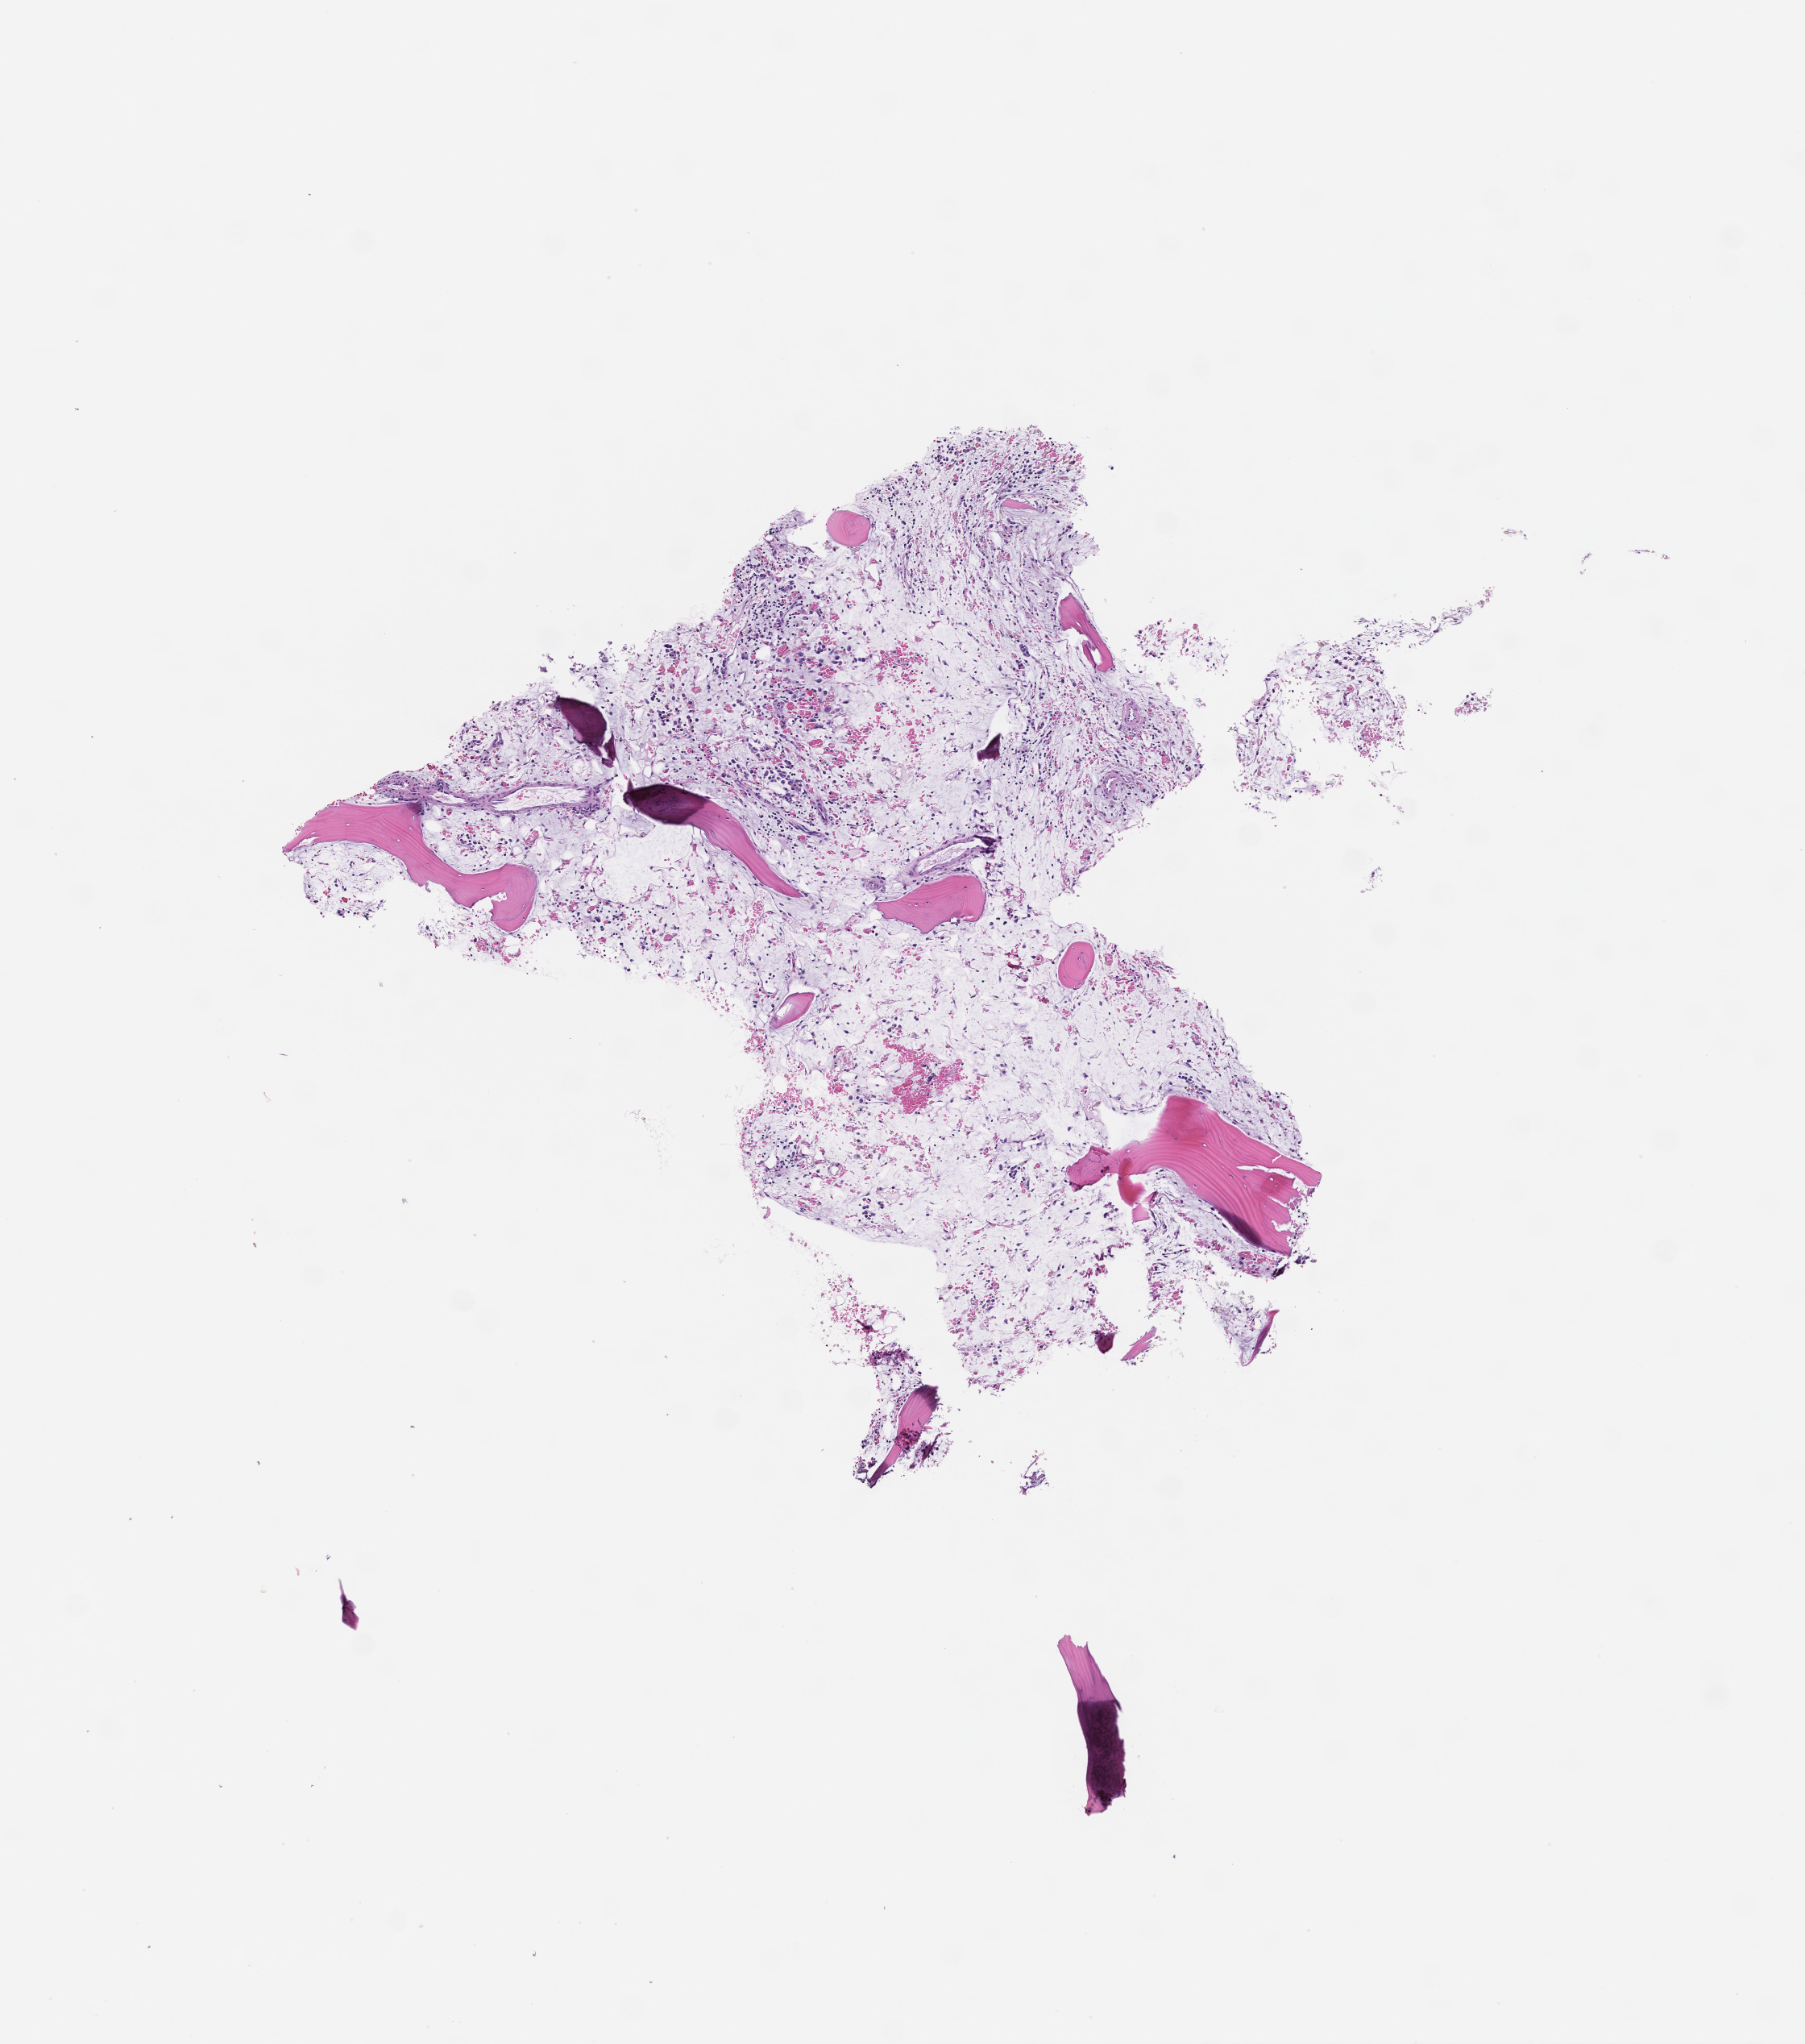
Whole-slide image, hematoxylin and eosin (H&E) stain — a low-resolution overview of the entire scanned area, about 4.5 x 5.1 mm. Formalin-fixed, paraffin-embedded (FFPE) tissue. Tissue site: bone marrow. Male patient.
- this section: primary tumour tissue
- diagnosis: Acute Myeloid Leukemia Not Otherwise Specified